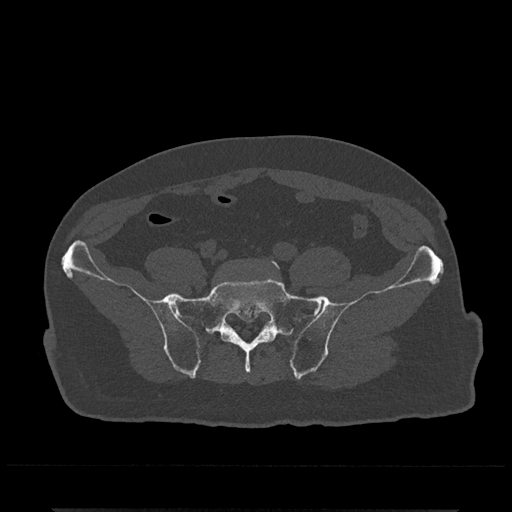
CT including the spine, one axial slice; position 29 of 797 along the scan axis; 120 kVp; bone window (W 1800 / L 400 HU); 0.5 mm slice thickness; 512 × 512 image matrix, field of view 393 × 393 mm. Male patient, age 67 years. Case-level facts recorded for this patient, not image findings: primary cancer: prostate.
Outlined on this slice (semi-automatically segmented with operator editing):
- L5 vertebra: bounding box (x1, y1, x2, y2) in pixels: (270, 260, 280, 269)